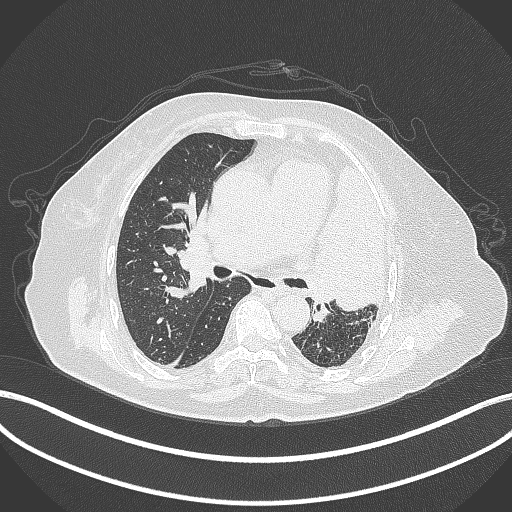
Chest CT, one axial slice; slice 224 of 399 in the series (ordered by position); reconstruction kernel B70f; 120 kVp; lung window (W 1500 / L -600 HU); 1 mm slice thickness; 512 × 512 image matrix. Female patient, age 75 years. Case-level facts recorded for this patient, not image findings: clinical TNM (as recorded): T3 N3 M1.
Annotated regions visible in this slice (bounding box drawn by a radiologist):
- lung tumour (recorded histology: adenocarcinoma): box from (x=302, y=152) to (x=391, y=311) px